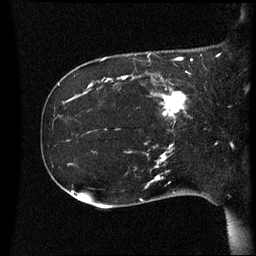
Breast MRI (dynamic contrast-enhanced), one sagittal slice. Position 15 of 60 along the scan axis. Dynamic contrast-enhanced series, image 2 of 3 at this slice position (ordered by acquisition). 1.5 T. TE 4.2 ms, TR 8.4 ms. 2.2 mm slice thickness. 256 × 256 image matrix. Female patient, age 41 years. Case-level facts recorded for this patient, not image findings: setting: breast cancer imaged before/during neoadjuvant chemotherapy; receptor status: HER2-positive.
Outlined on this slice (semi-automatic segmentation, software-assisted and operator-edited):
- analysis volume of interest (the breast-tissue region the enhancement analysis was run in; not a lesion): bounding box [x1, y1, x2, y2] px = [122, 80, 196, 123]
- tumour enhancement mask (voxels above the 70 % enhancement threshold inside the analysis volume of interest): [161, 90, 187, 119]